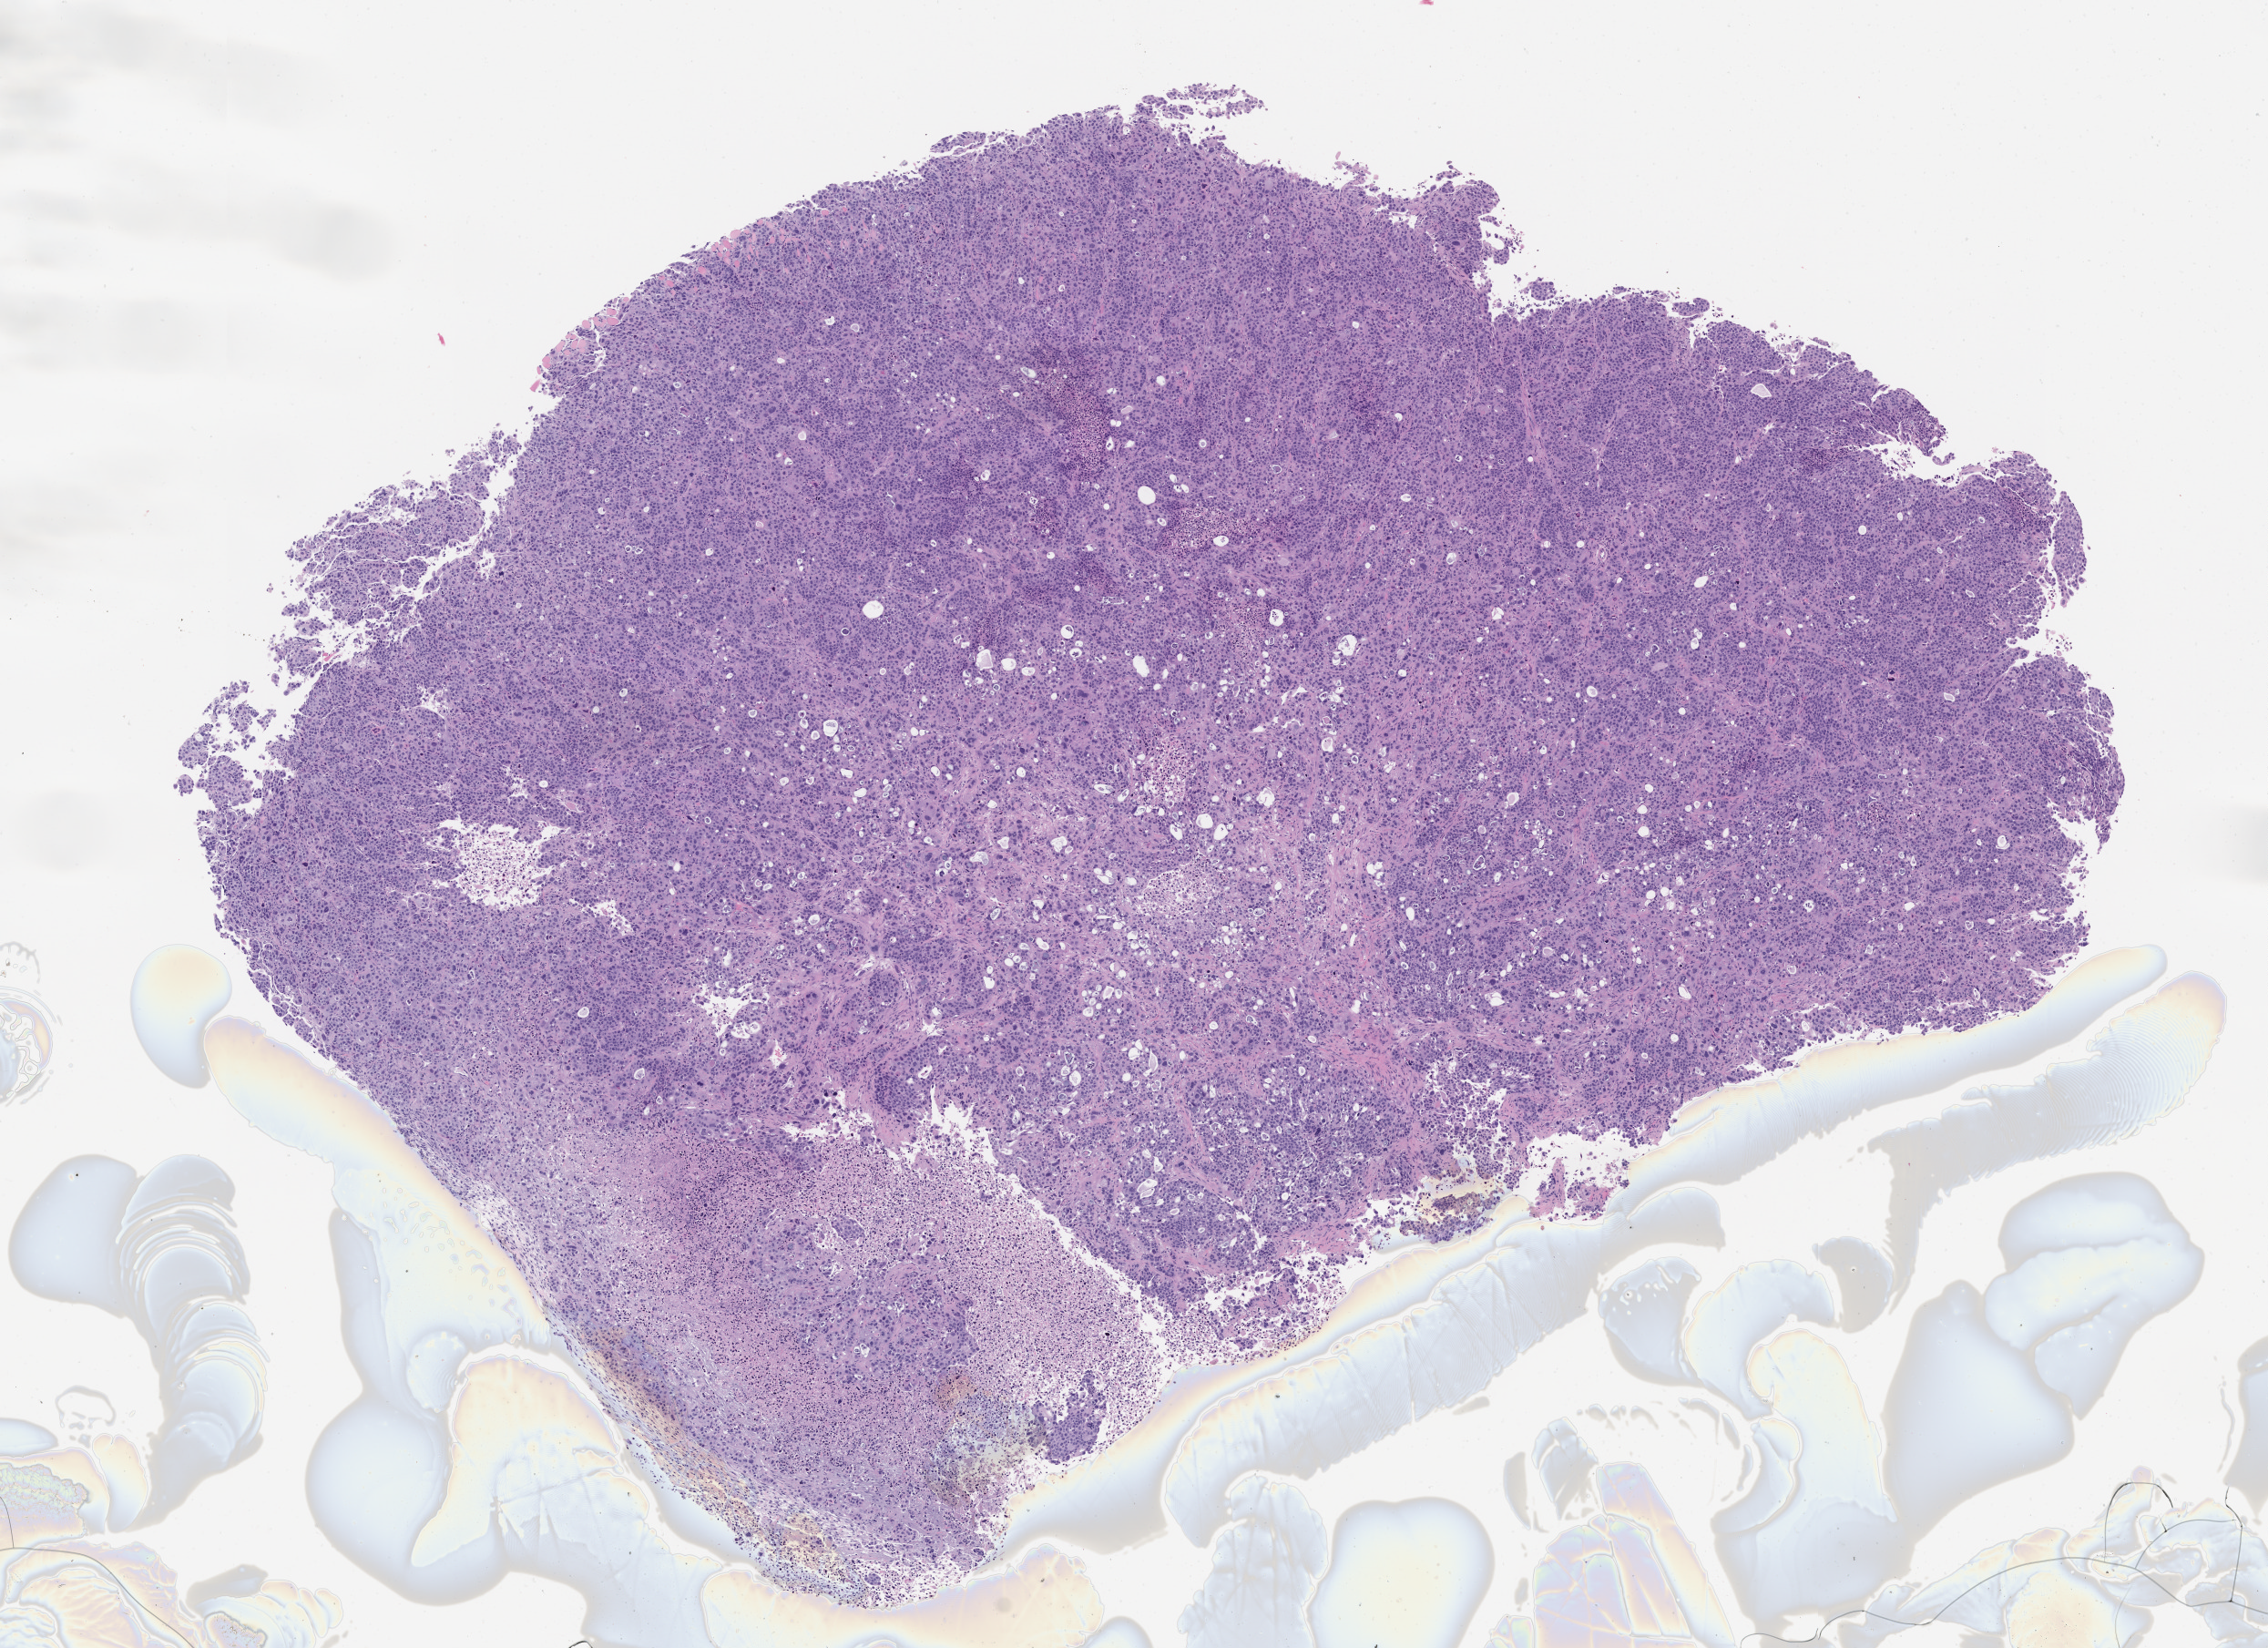
Whole-slide image, hematoxylin and eosin (H&E): patient-derived xenograft (human tumor grown in a mouse), passage 4, a low-resolution overview of the entire scanned area, about 10.0 x 7.3 mm; FFPE section; originating tumor site category: bladder.
Originating patient diagnosis: Urothelial Carcinoma.